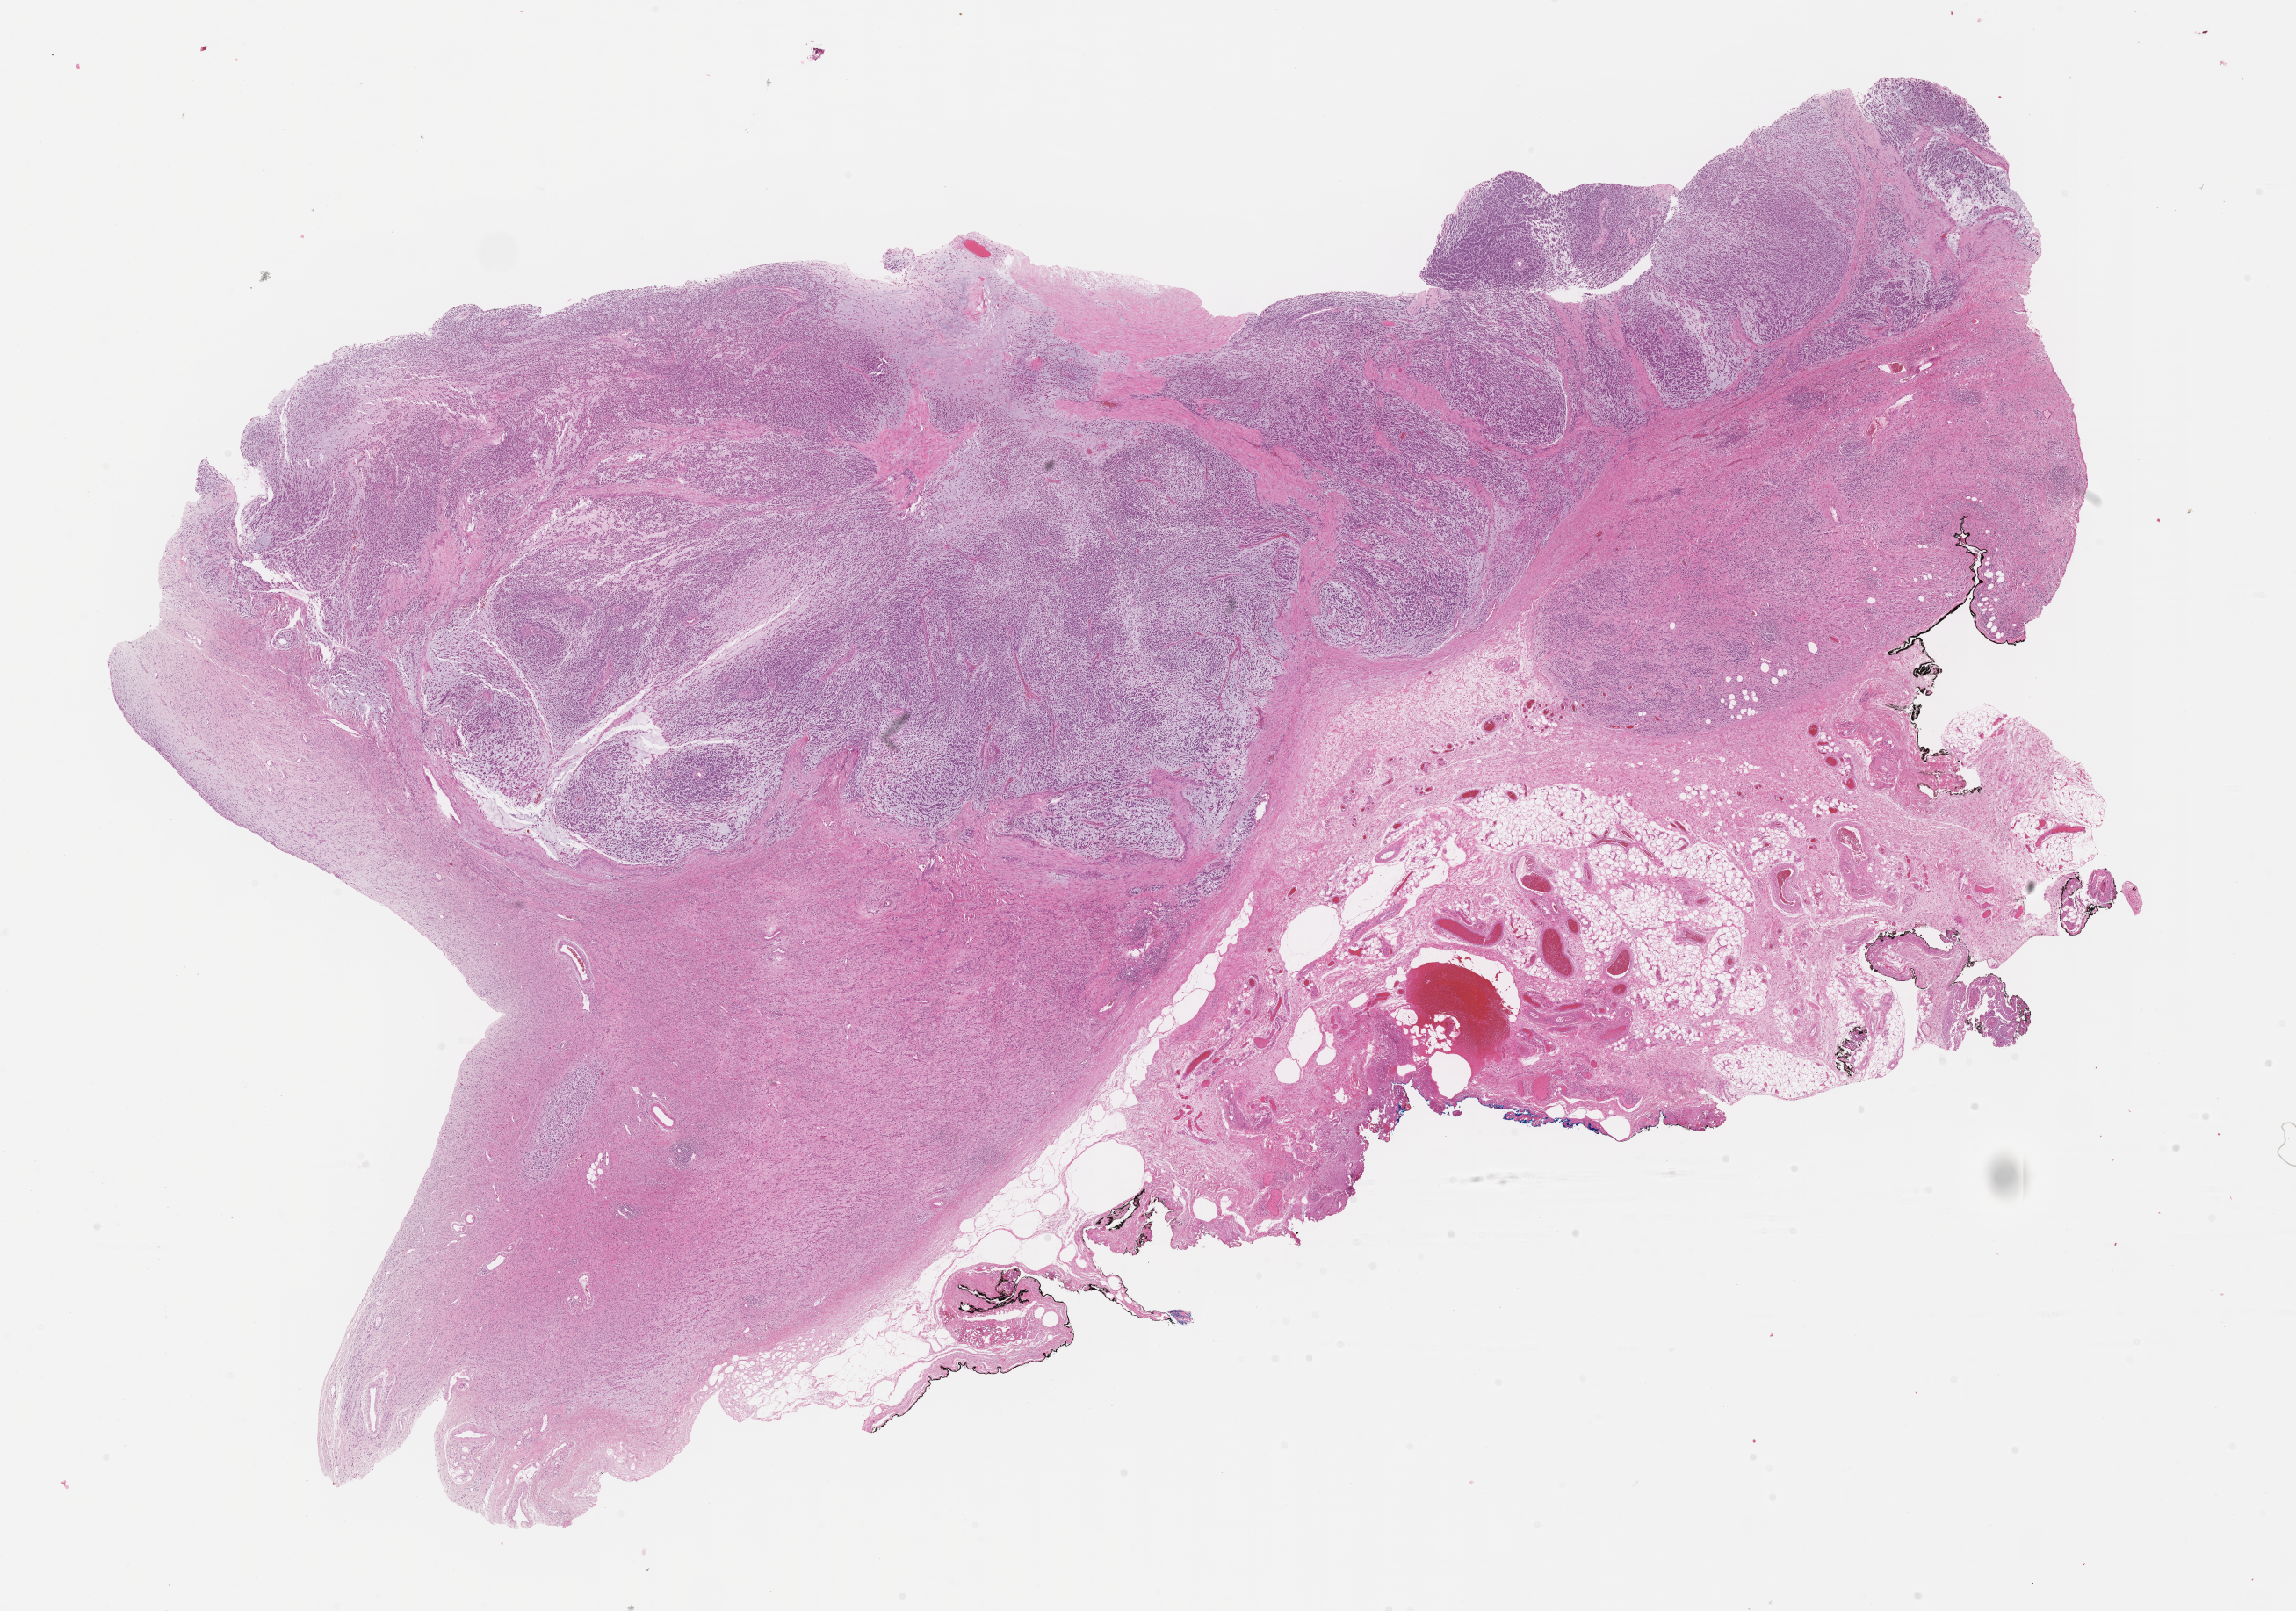
Hematoxylin and eosin (H&E) whole-slide image of tumor tissue — whole scanned area (about 21.1 x 14.8 mm) shown as a low-resolution overview, FFPE section, sample anatomic site: paratesticular, left. Male patient, age at diagnosis 3.7 years.
Stage (as recorded): 1. Diagnosis: rhabdomyosarcoma; histological classification: embryonal rhabdomyosarcoma.